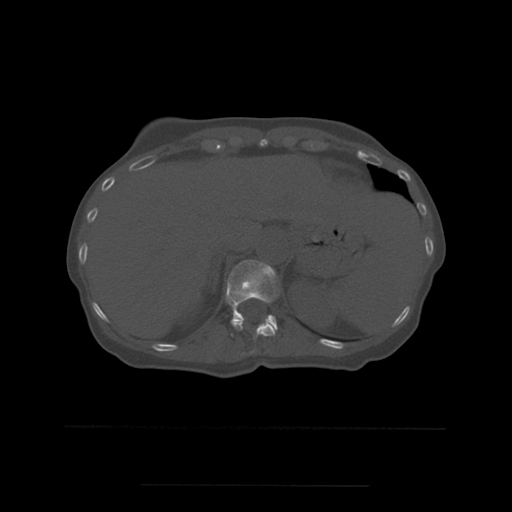
CT including the spine, one axial slice; position 270 of 544 along the scan axis; bone window (W 1800 / L 400 HU); 1.25 mm slice thickness; 512 × 512 image matrix. Patient age 58 years. From the clinical record (not read from this slice): primary cancer: lung.
Outlined on this slice (semi-automatic segmentation, software-assisted and operator-edited):
- T11 vertebra: bounding box [x1, y1, x2, y2] px = [231, 319, 275, 353]
- T12 vertebra: [226, 260, 278, 337]